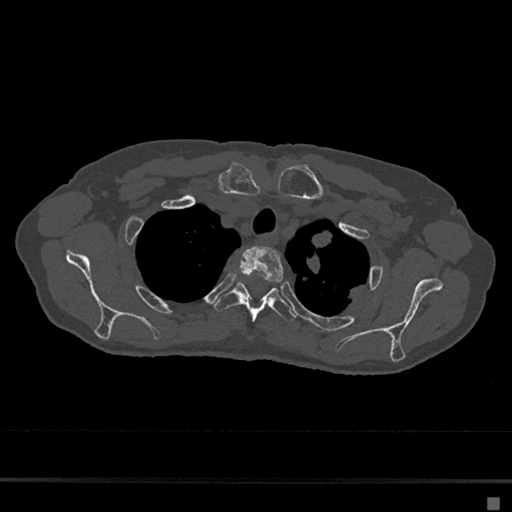
CT including the spine, one axial slice. Position 556 of 797 along the scan axis. Reconstruction kernel Br40s/3. Bone window (W 1800 / L 400 HU). 0.5 mm slice thickness. 512 × 512 image matrix, field of view 360 × 360 mm. Female patient, age 68 years. Case-level facts recorded for this patient, not image findings: primary cancer: renal.
Structures marked on this image (semi-automatically segmented with operator editing):
- T2 vertebra: bounding box (x1, y1, x2, y2) in pixels: (235, 246, 284, 295)
- T3 vertebra: (213, 282, 296, 323)